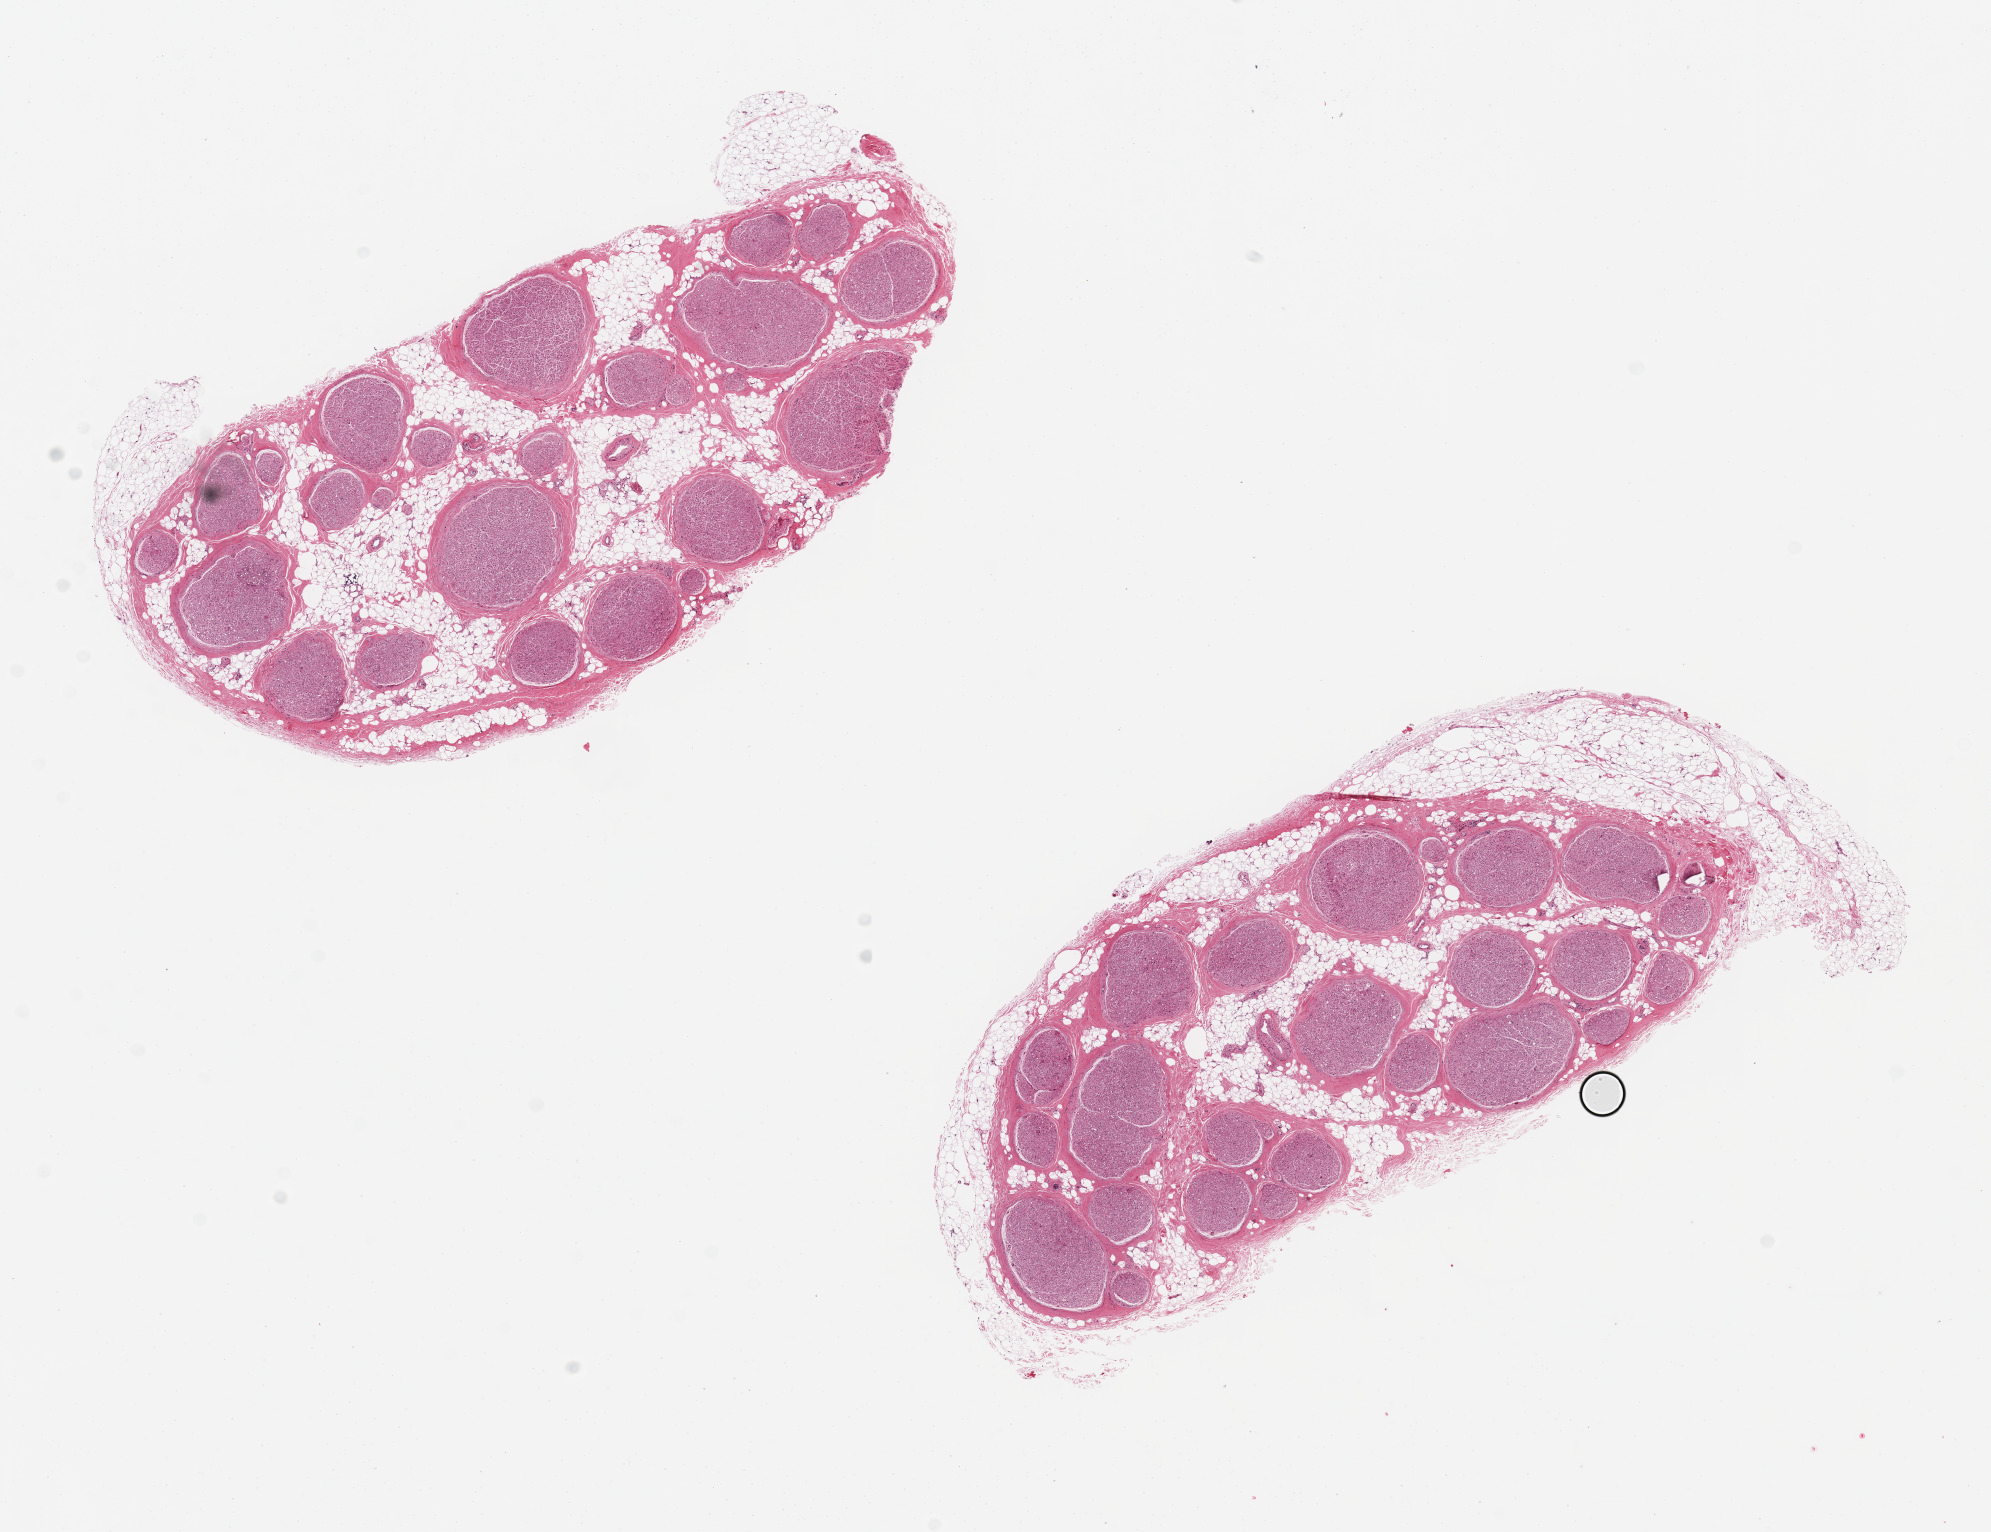
Whole-slide image, H&E stain, shown as a low-resolution overview of the whole scanned area (about 15.8 x 12.1 mm); PAXgene-fixed, paraffin-embedded tissue; sampled site (target tissue): tibial nerve; tissue donor sample. Donor sex: female.
Review note (as recorded): 2 aliquots, ~7x3mm, ~20% interspersed and adherent fat.